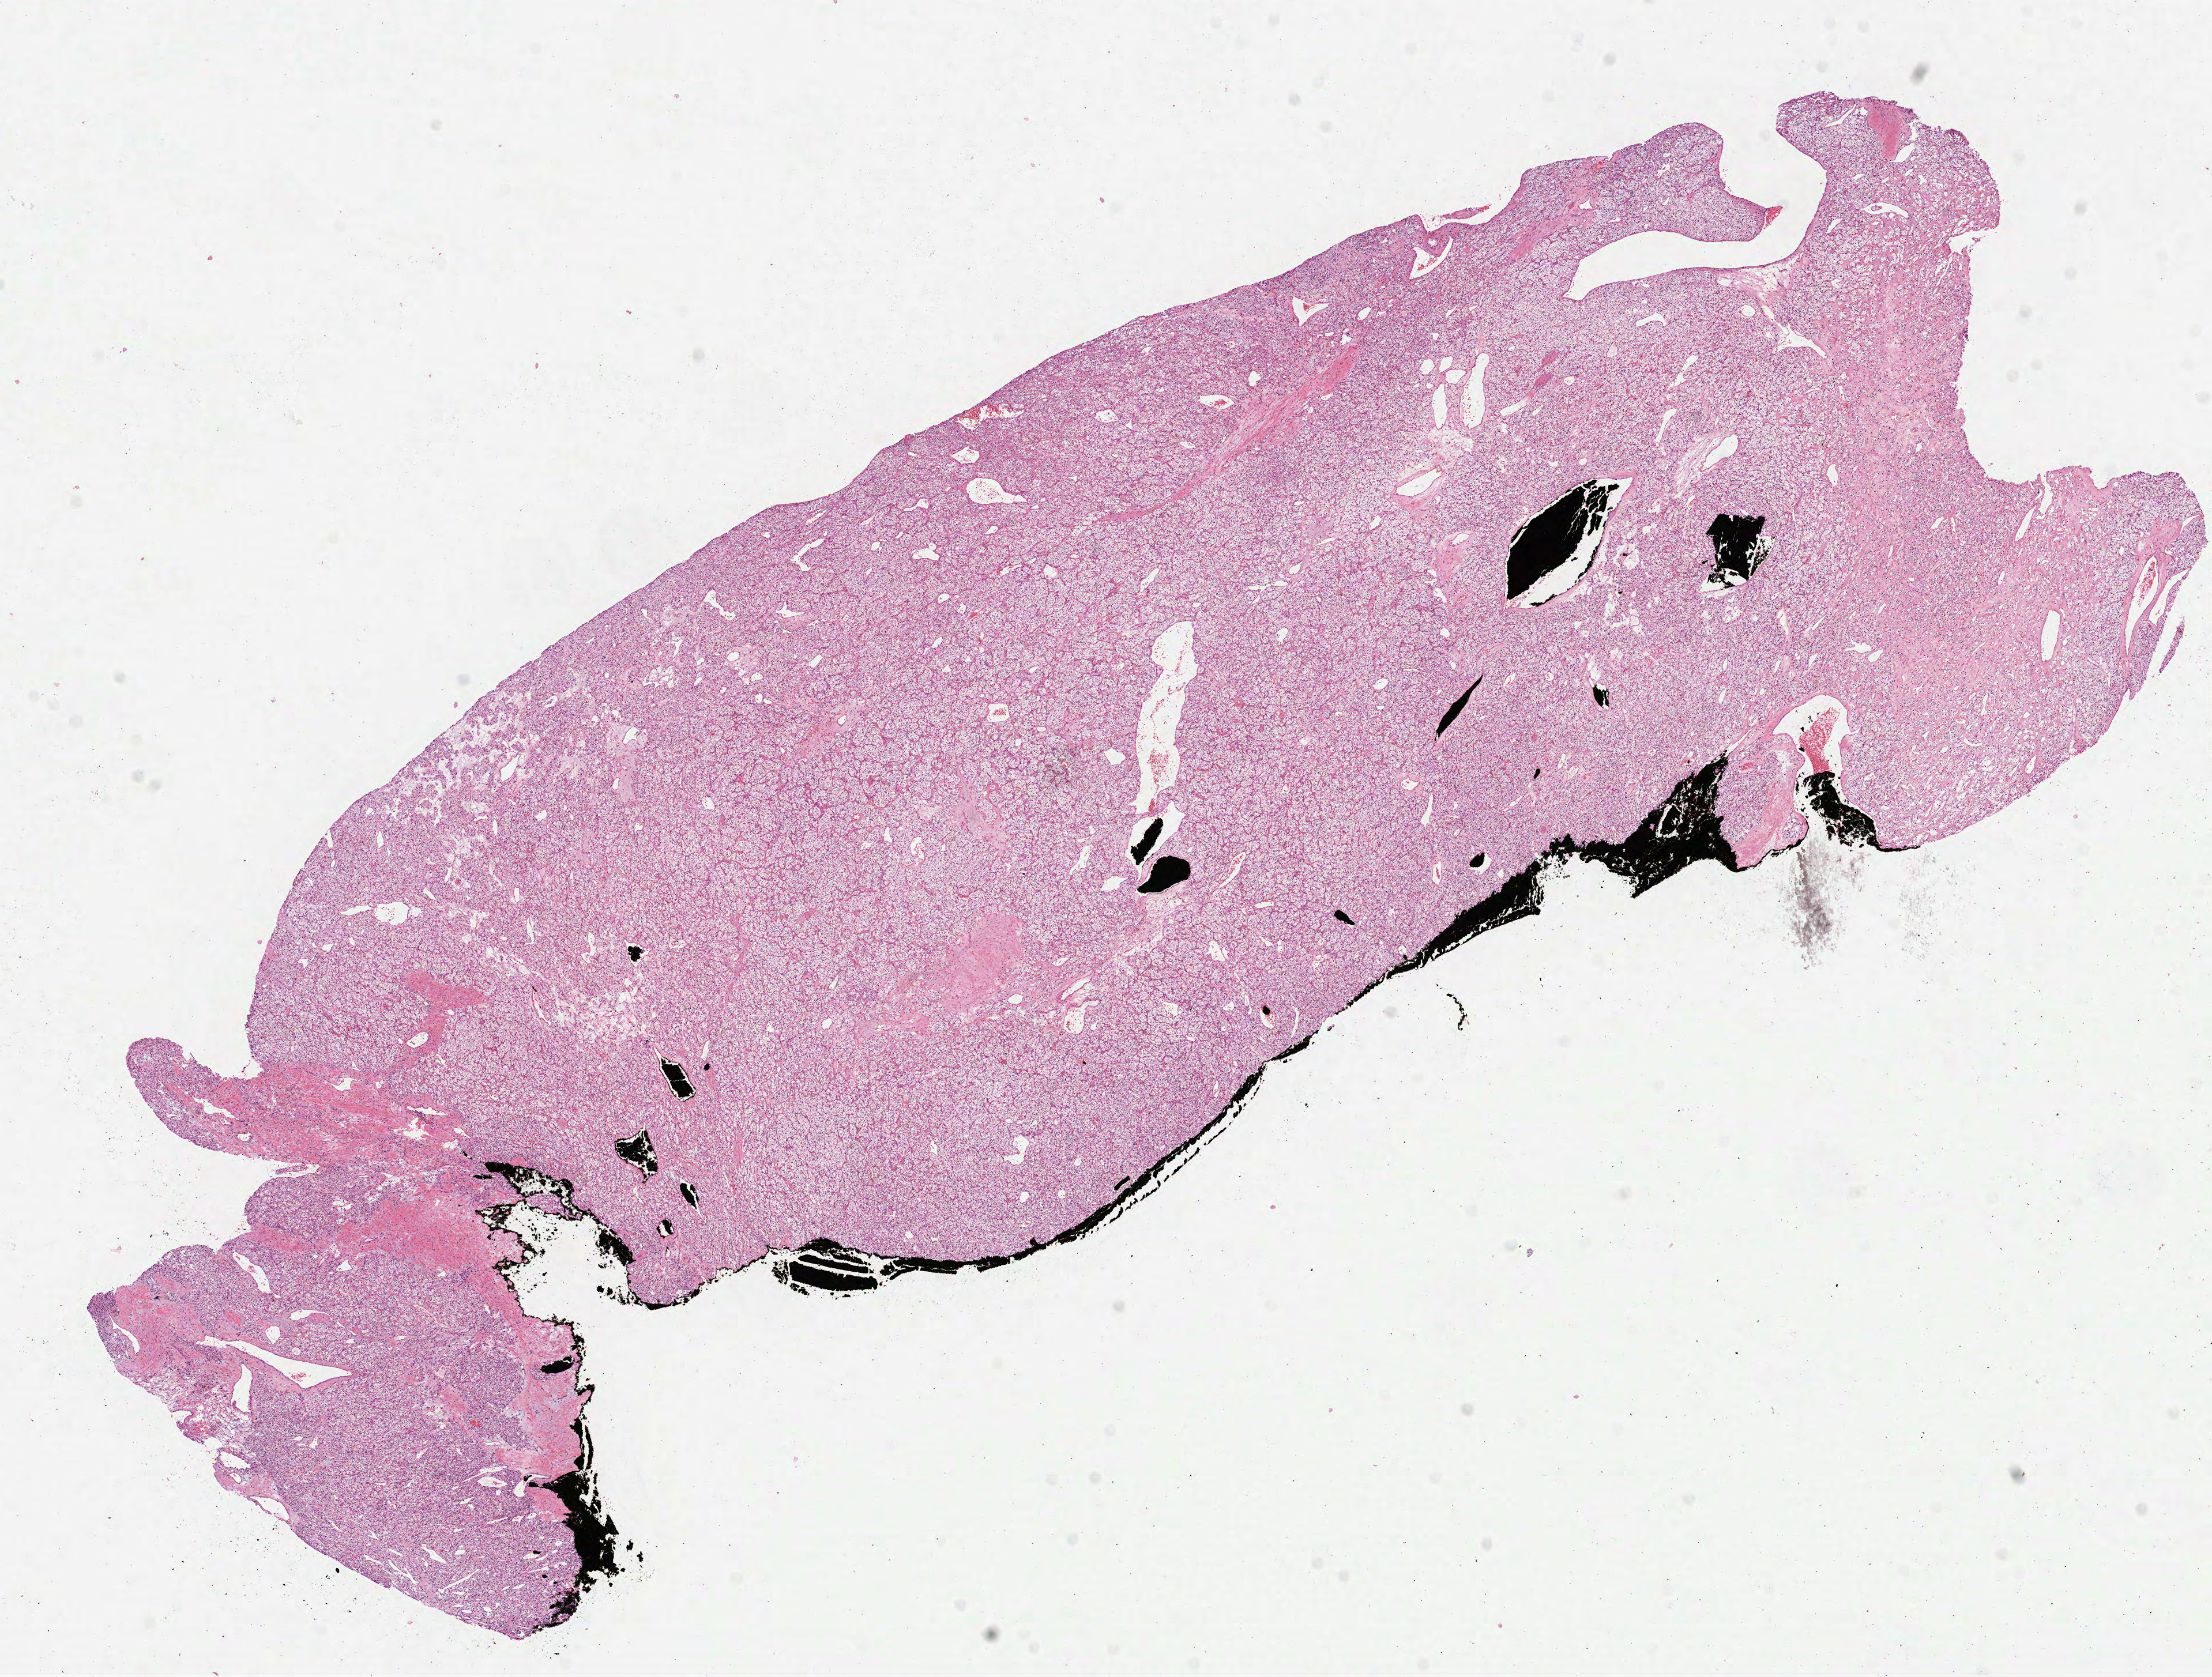
Digitized H&E tissue section (whole slide), whole scanned area (about 15.5 x 11.7 mm, from a 40x scan) shown as a low-resolution overview. FFPE section. Kidney, primary tumour sample. Patient: female, age at initial diagnosis 52 years. Histologic grade: G1 (well differentiated).
AJCC pathologic stage: I. Diagnosis: Clear cell adenocarcinoma, NOS.